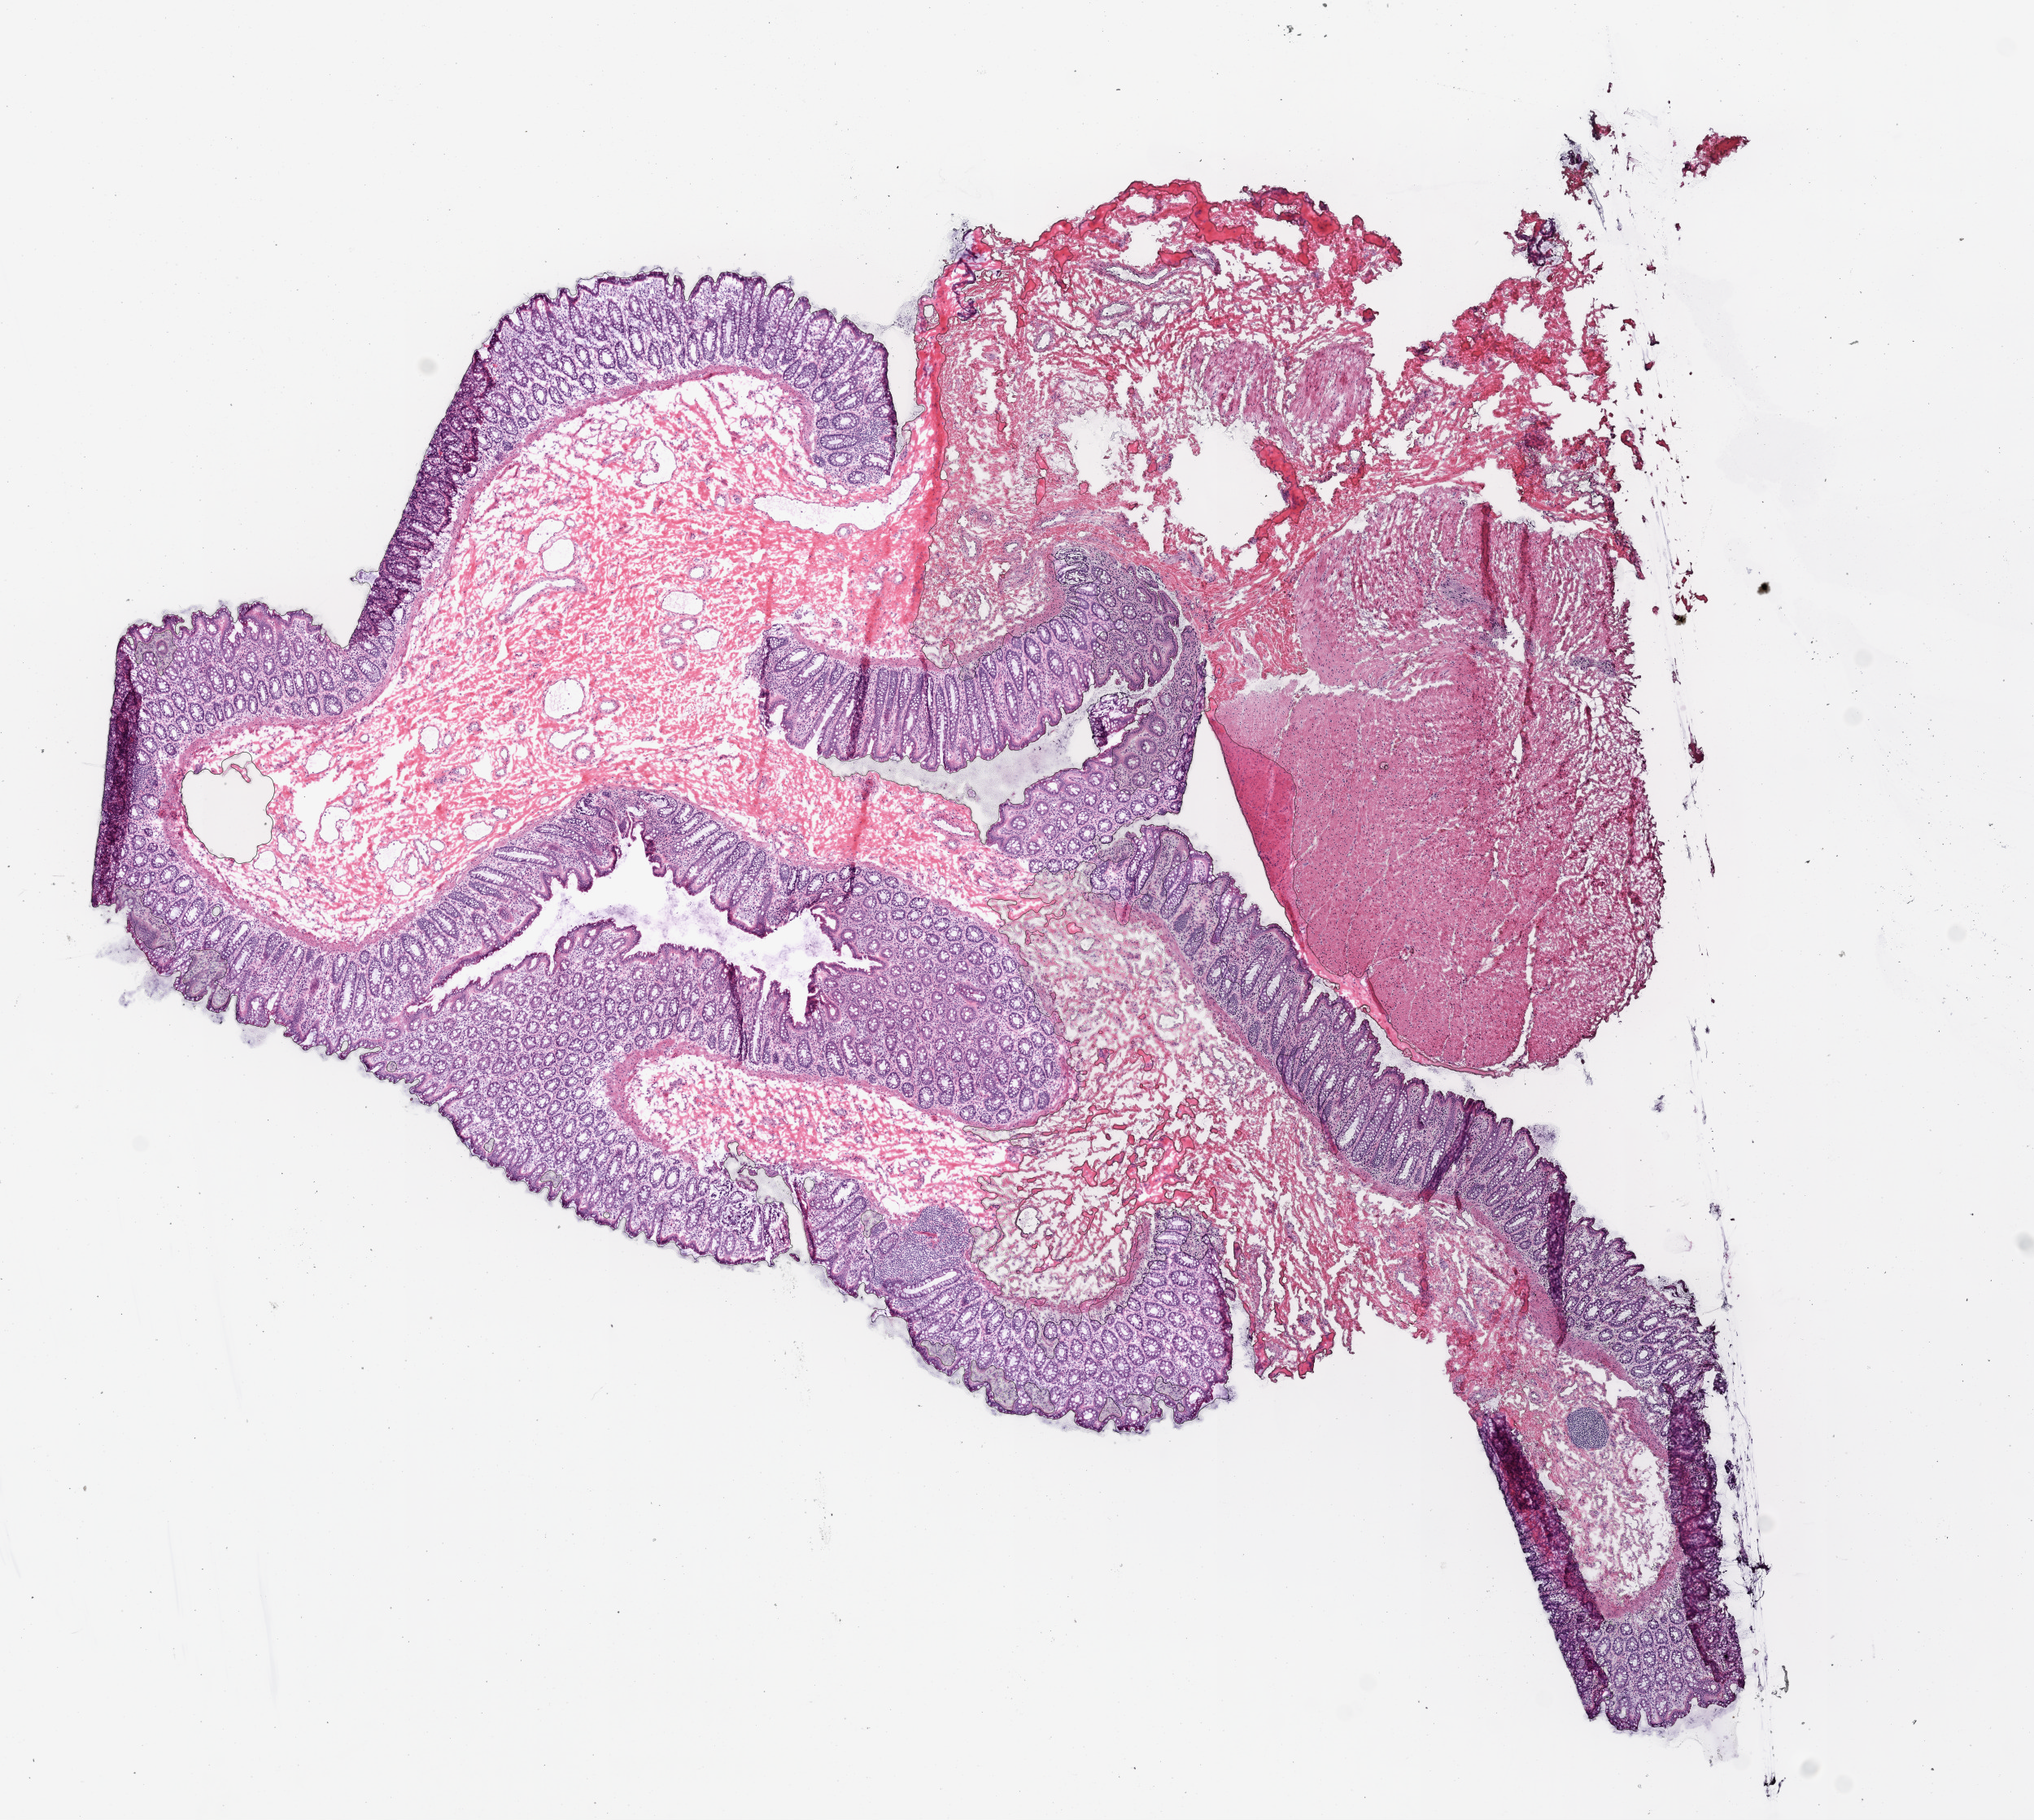
Whole-slide histology image, H&E-stained, whole scanned area (about 10.0 x 9.0 mm, acquisition: 20x scan) shown as a low-resolution overview; frozen section from the top of the tissue portion; solid tissue normal (non-tumour tissue) sample from the colon. Male patient; age at initial diagnosis 58 years.
- this section: solid tissue normal sample (biorepository sample class)
- patient diagnosis: Adenocarcinoma, NOS (rectosigmoid junction)